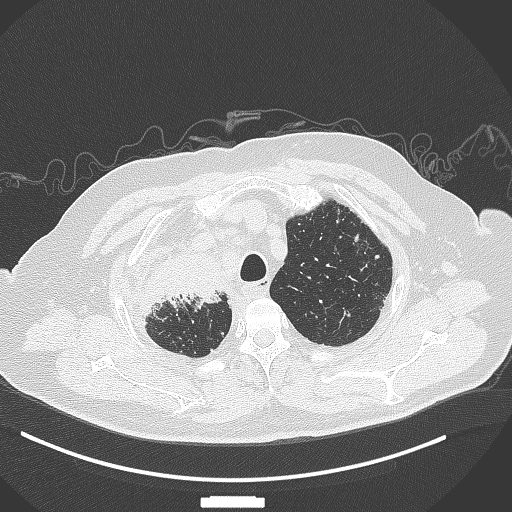
Chest CT, one axial slice. Slice 305 of 384 in the series (ordered by position). 120 kVp. Lung window (W 1500 / L -600 HU). 1 mm slice thickness. 512 × 512 image matrix. Patient: male, 69 years. Case-level facts recorded for this patient, not image findings: clinical TNM (as recorded): T4 N3 M1.
Outlined on this slice (rectangle marked by the reading radiologist):
- lung tumour (recorded histology: adenocarcinoma): bounding box <133,249,234,321> (left, top, right, bottom; pixels)